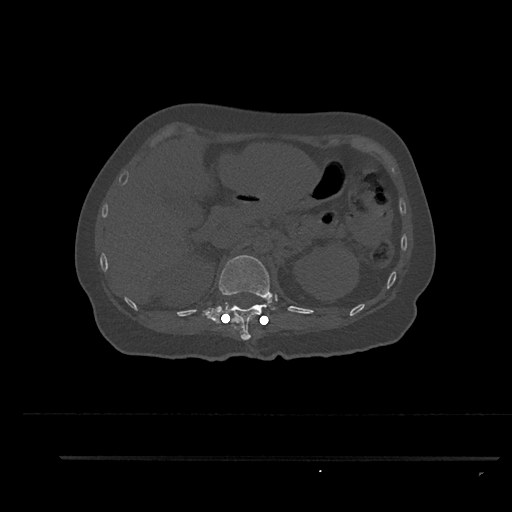
CT including the spine, one axial slice. Position 251 of 797 along the scan axis. Reconstruction kernel Br40s/3. Bone window (W 1800 / L 400 HU). 512 × 512 image matrix, field of view 408 × 408 mm. Female patient, age 44 years. Case-level facts recorded for this patient, not image findings: primary cancer: renal; vertebrae with lytic lesions (as recorded): L1.
Outlined on this slice (semi-automatically segmented with operator editing):
- T12 vertebra: bounding box [x1, y1, x2, y2] px = [202, 255, 273, 340]